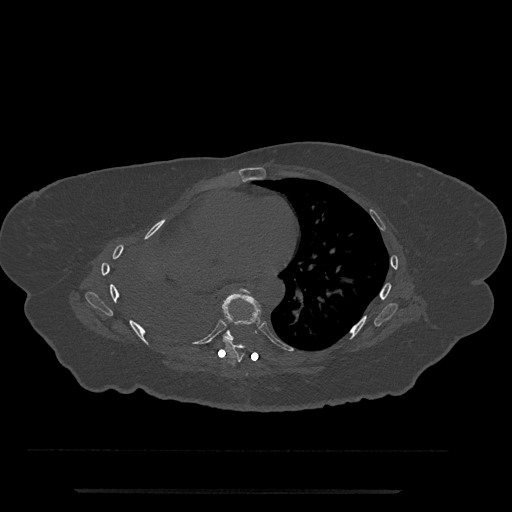
CT including the spine, one axial slice. Position 424 of 797 along the scan axis. Bone window (W 1800 / L 400 HU). 512 × 512 image matrix, field of view 440 × 440 mm. Female patient, age 51 years. Case-level facts recorded for this patient, not image findings: primary cancer: neuro; vertebrae with lytic lesions (as recorded): T8.
Annotated regions visible in this slice (semi-automatically segmented with operator editing):
- T7 vertebra: bounding box [x1, y1, x2, y2] px = [222, 289, 263, 363]
- T8 vertebra: [223, 290, 249, 341]